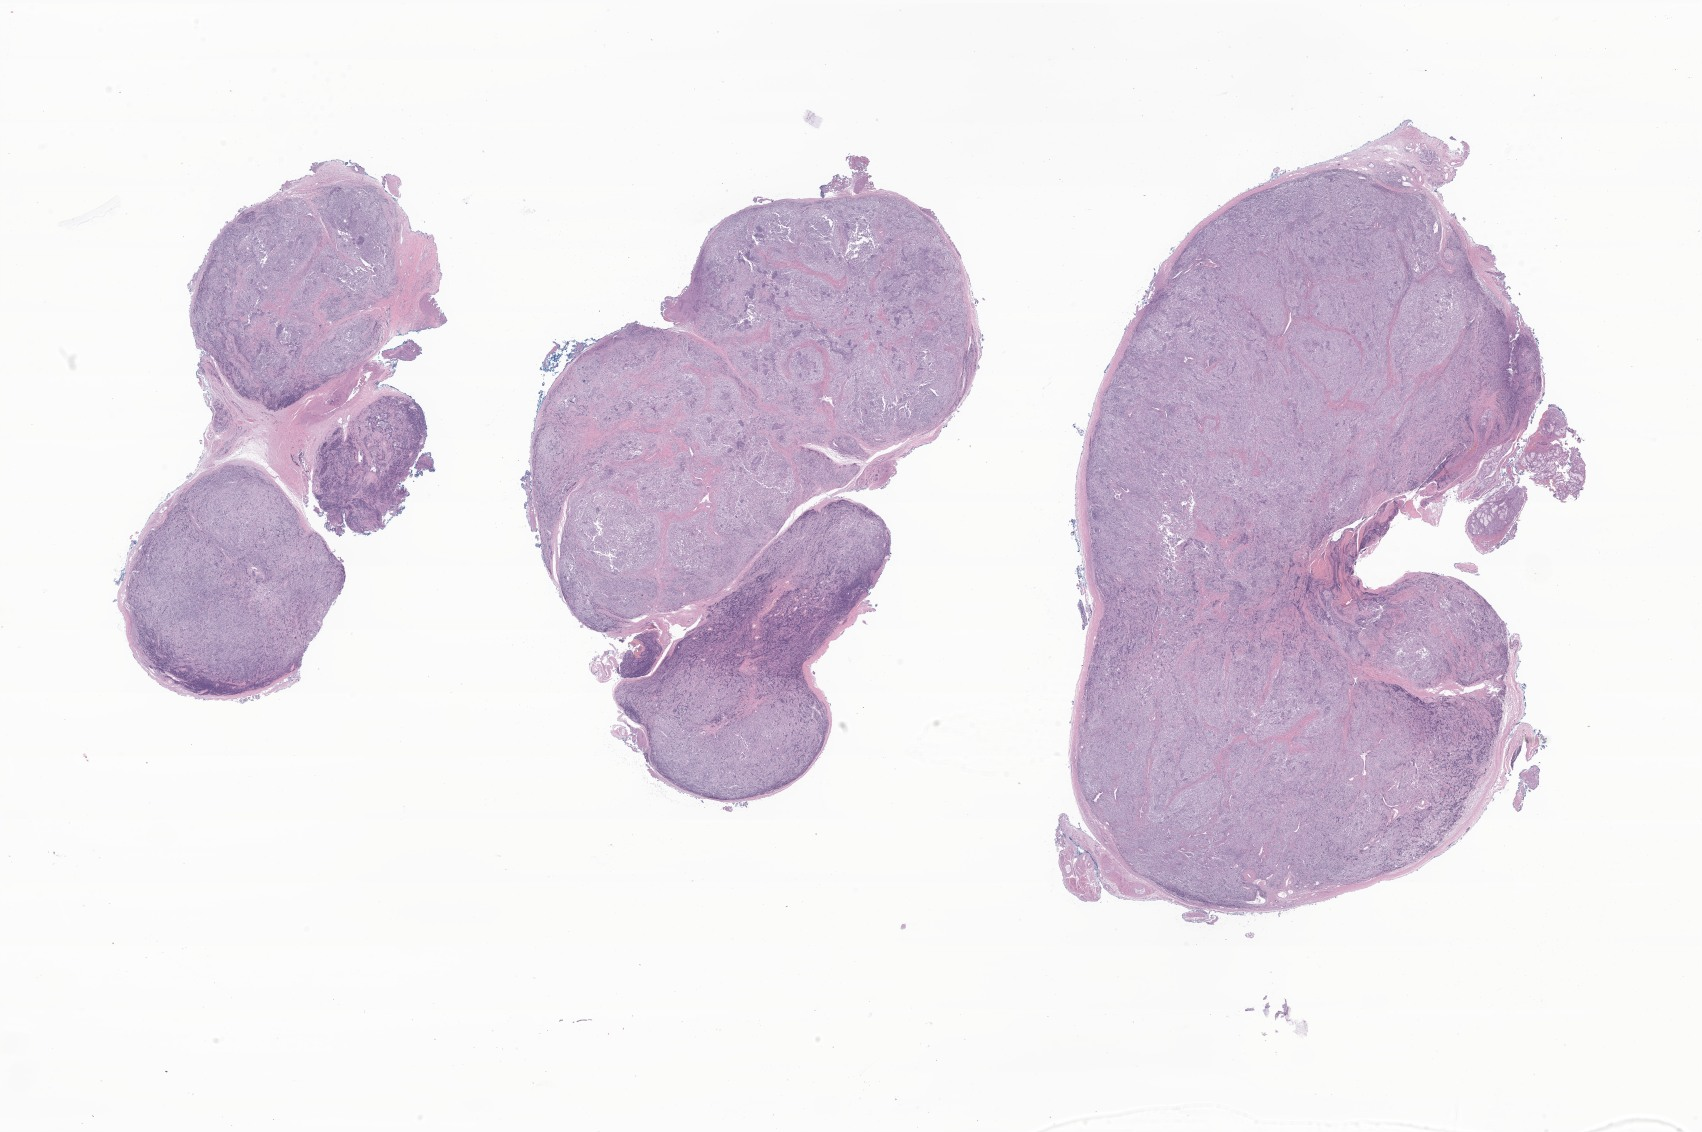
H&E whole-slide image of tumor tissue from the floor of mouth — shown as a low-resolution overview of the whole scanned area (about 28.7 x 19.1 mm), FFPE section. Patient: female, age 308 days.
Recorded diagnosis: Malignant tumor, spindle cell type.